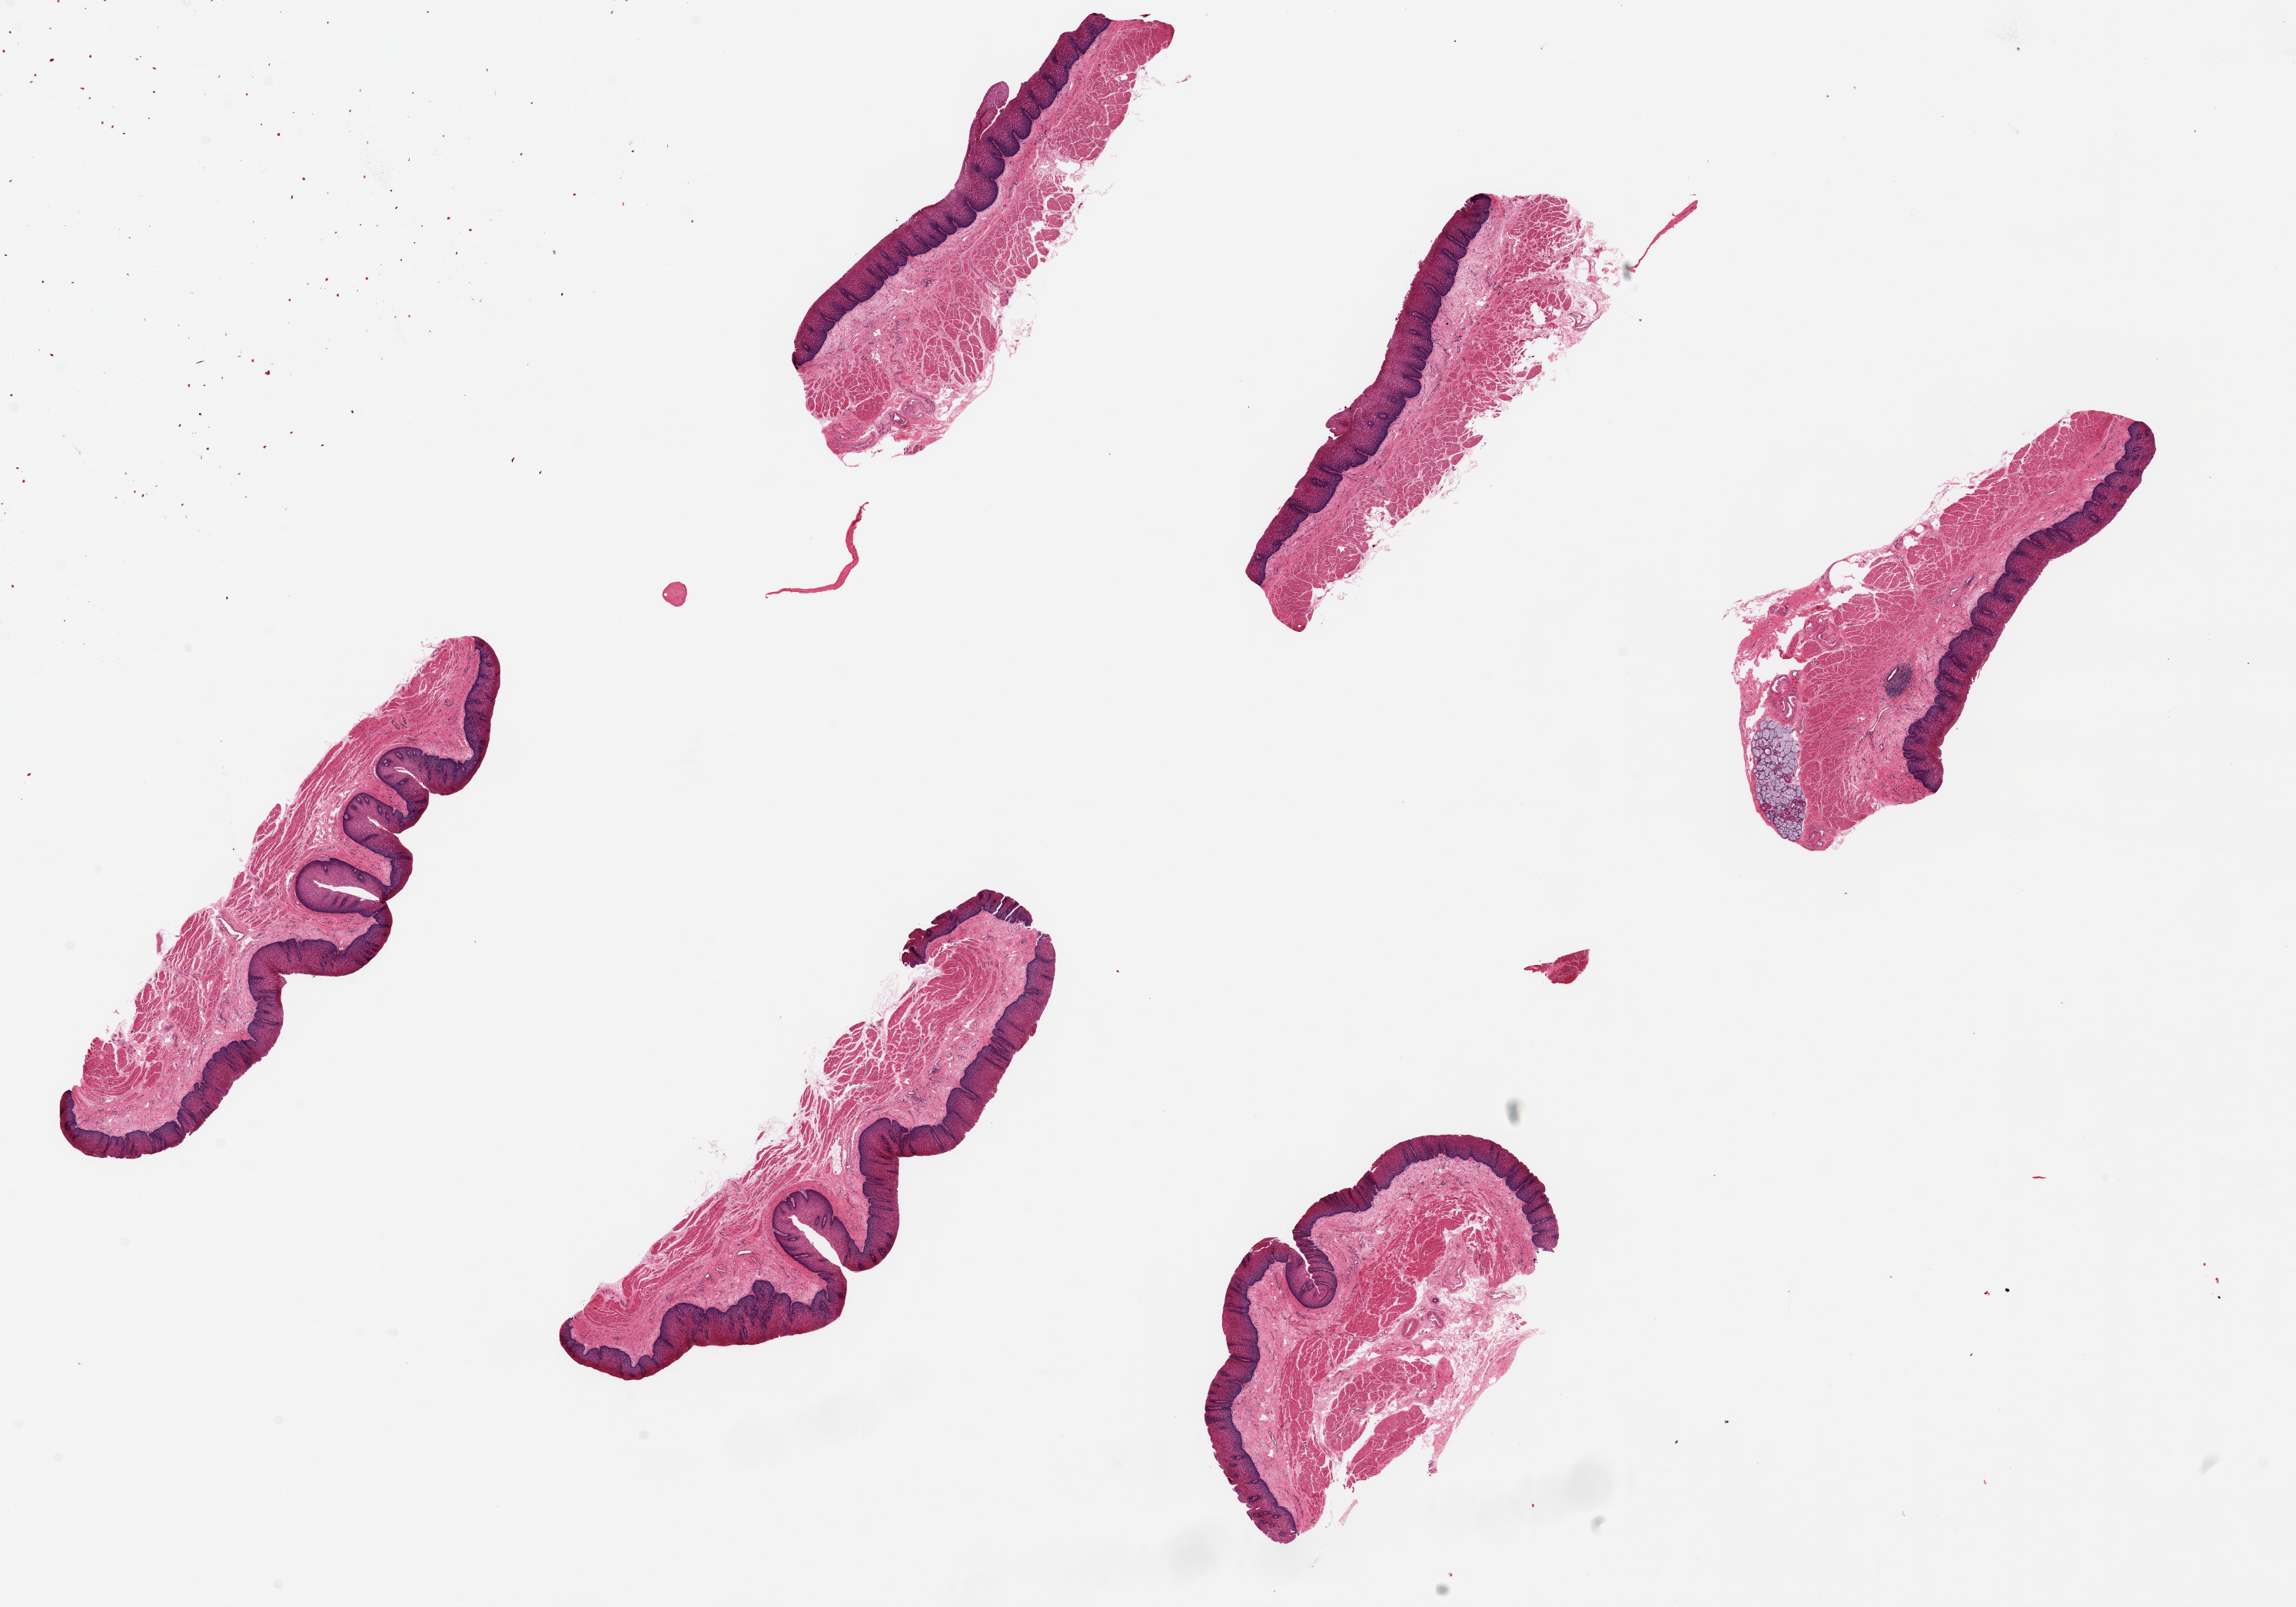
Hematoxylin and eosin (H&E) whole-slide image — low-resolution overview of the scanned area, about 23.6 x 16.5 mm (from a 20x scan), PAXgene-fixed, paraffin-embedded tissue, section of esophageal mucous membrane (target tissue), donor tissue sample.
* pathologist's review note for this sample: 6 pieces, up to 7x2mm; Well sampled mucosa